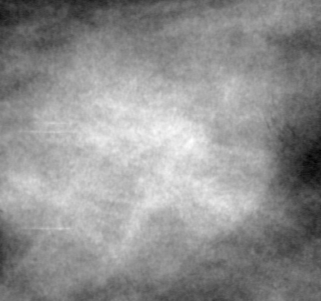
Crop from a digitized film mammogram around one marked abnormality, right breast, CC view.
Finding: mass, shape lobulated, margins ill defined; BI-RADS assessment category 4; subtlety rating 3 on a 1 (subtle) to 5 (obvious) scale; pathology result (as recorded, not read from the image): benign.